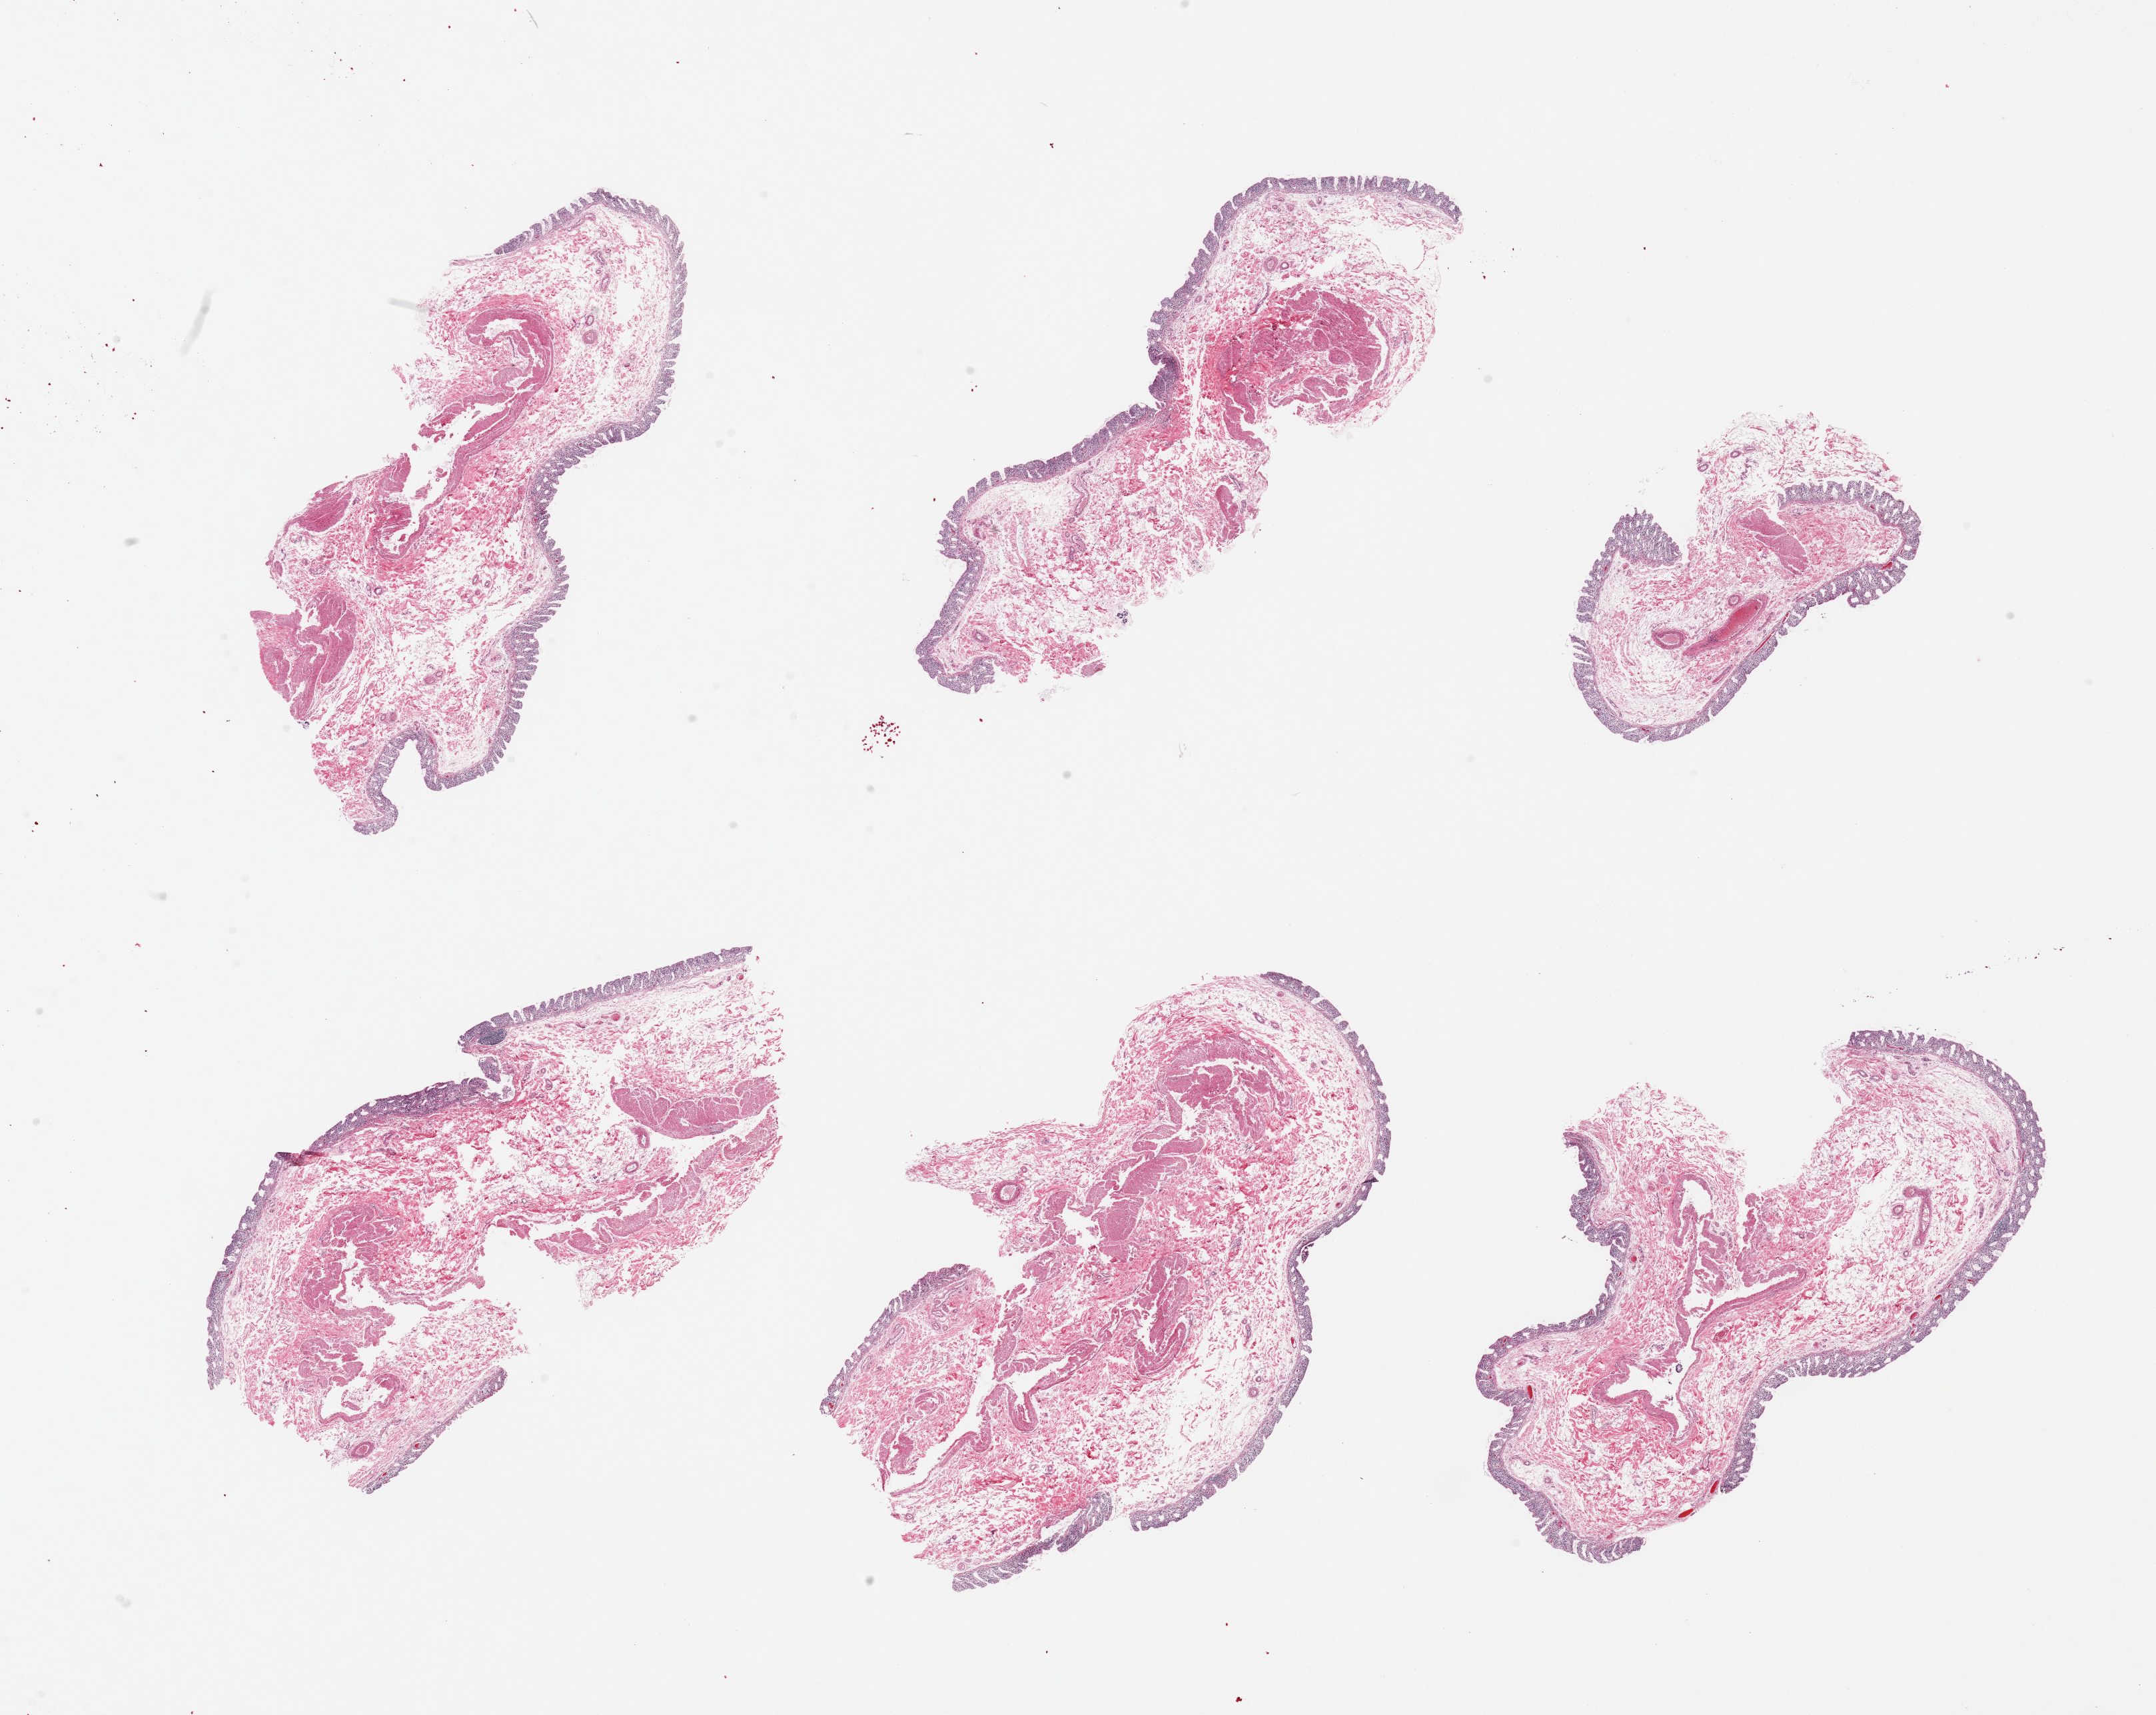
Haematoxylin and eosin whole-slide image — a low-resolution overview of the entire scanned area, about 25.6 x 20.4 mm (slide scanned at 20x), PAXgene-fixed, paraffin-embedded tissue, sampled site (target tissue): ileum, tissue donor sample.
- reviewer comment on this tissue sample: 6 pieces, advanced autolysis; insufficient target lymphoid aggregates present (<1%)